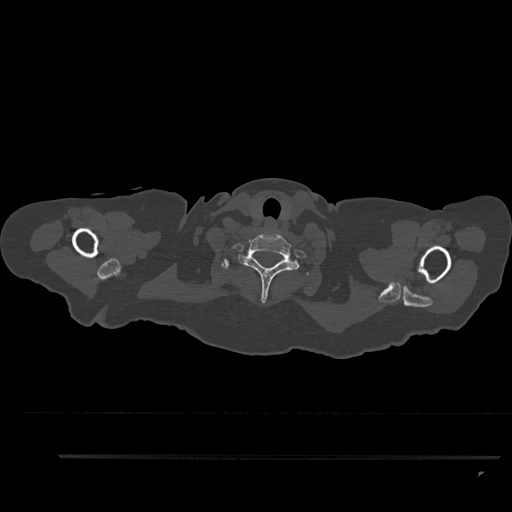
CT including the spine, one axial slice. Slice 790 of 797 in the series (ordered by position). Reconstruction kernel Br40s/3. 120 kVp. Bone window (W 1800 / L 400 HU). 0.5 mm slice thickness. 512 × 512 image matrix. Patient: female, 44 years. From the clinical record (not read from this slice): primary cancer: renal.
Structures marked on this image (semi-automatically segmented with operator editing):
- T1 vertebra: bounding box <222,259,309,275> (left, top, right, bottom; pixels)